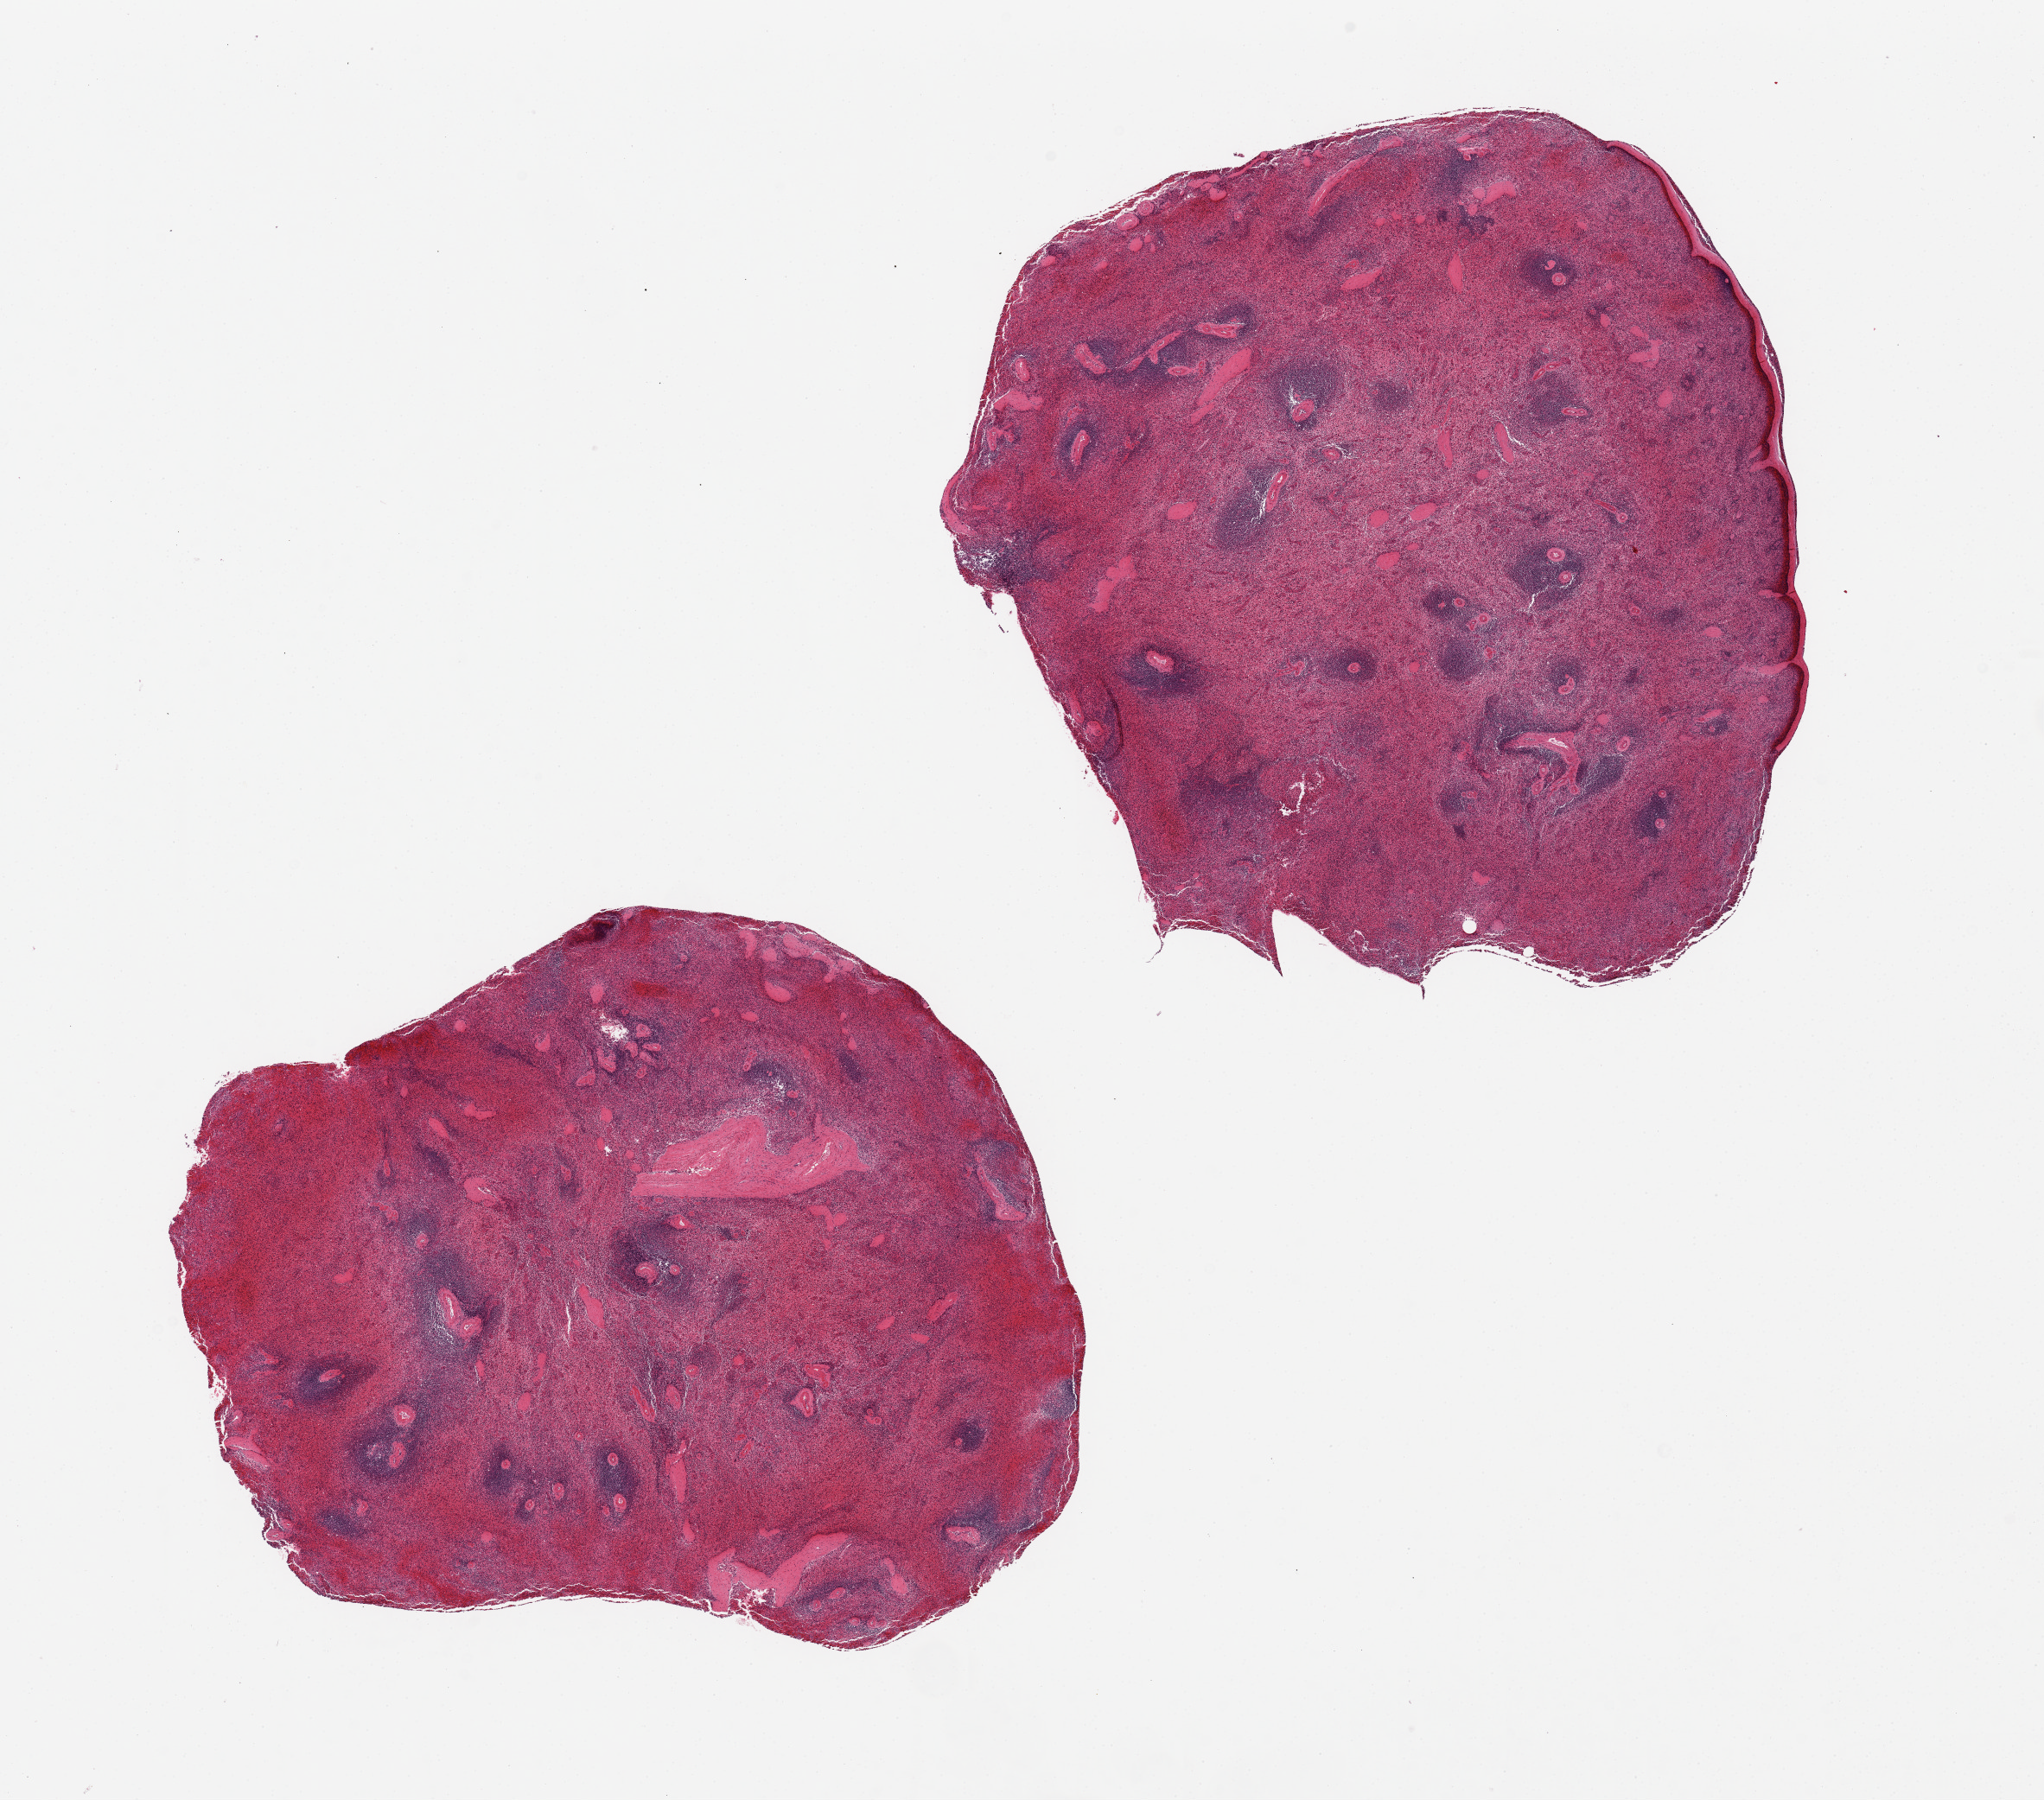
Whole-slide image, haematoxylin and eosin stain, shown as a low-resolution overview of the whole scanned area (about 18.7 x 16.5 mm). PAXgene-fixed, paraffin-embedded tissue. Sampled site (target tissue): spleen. Donor tissue sample.
Review note (as recorded): 2 pieces, moderate congestion.